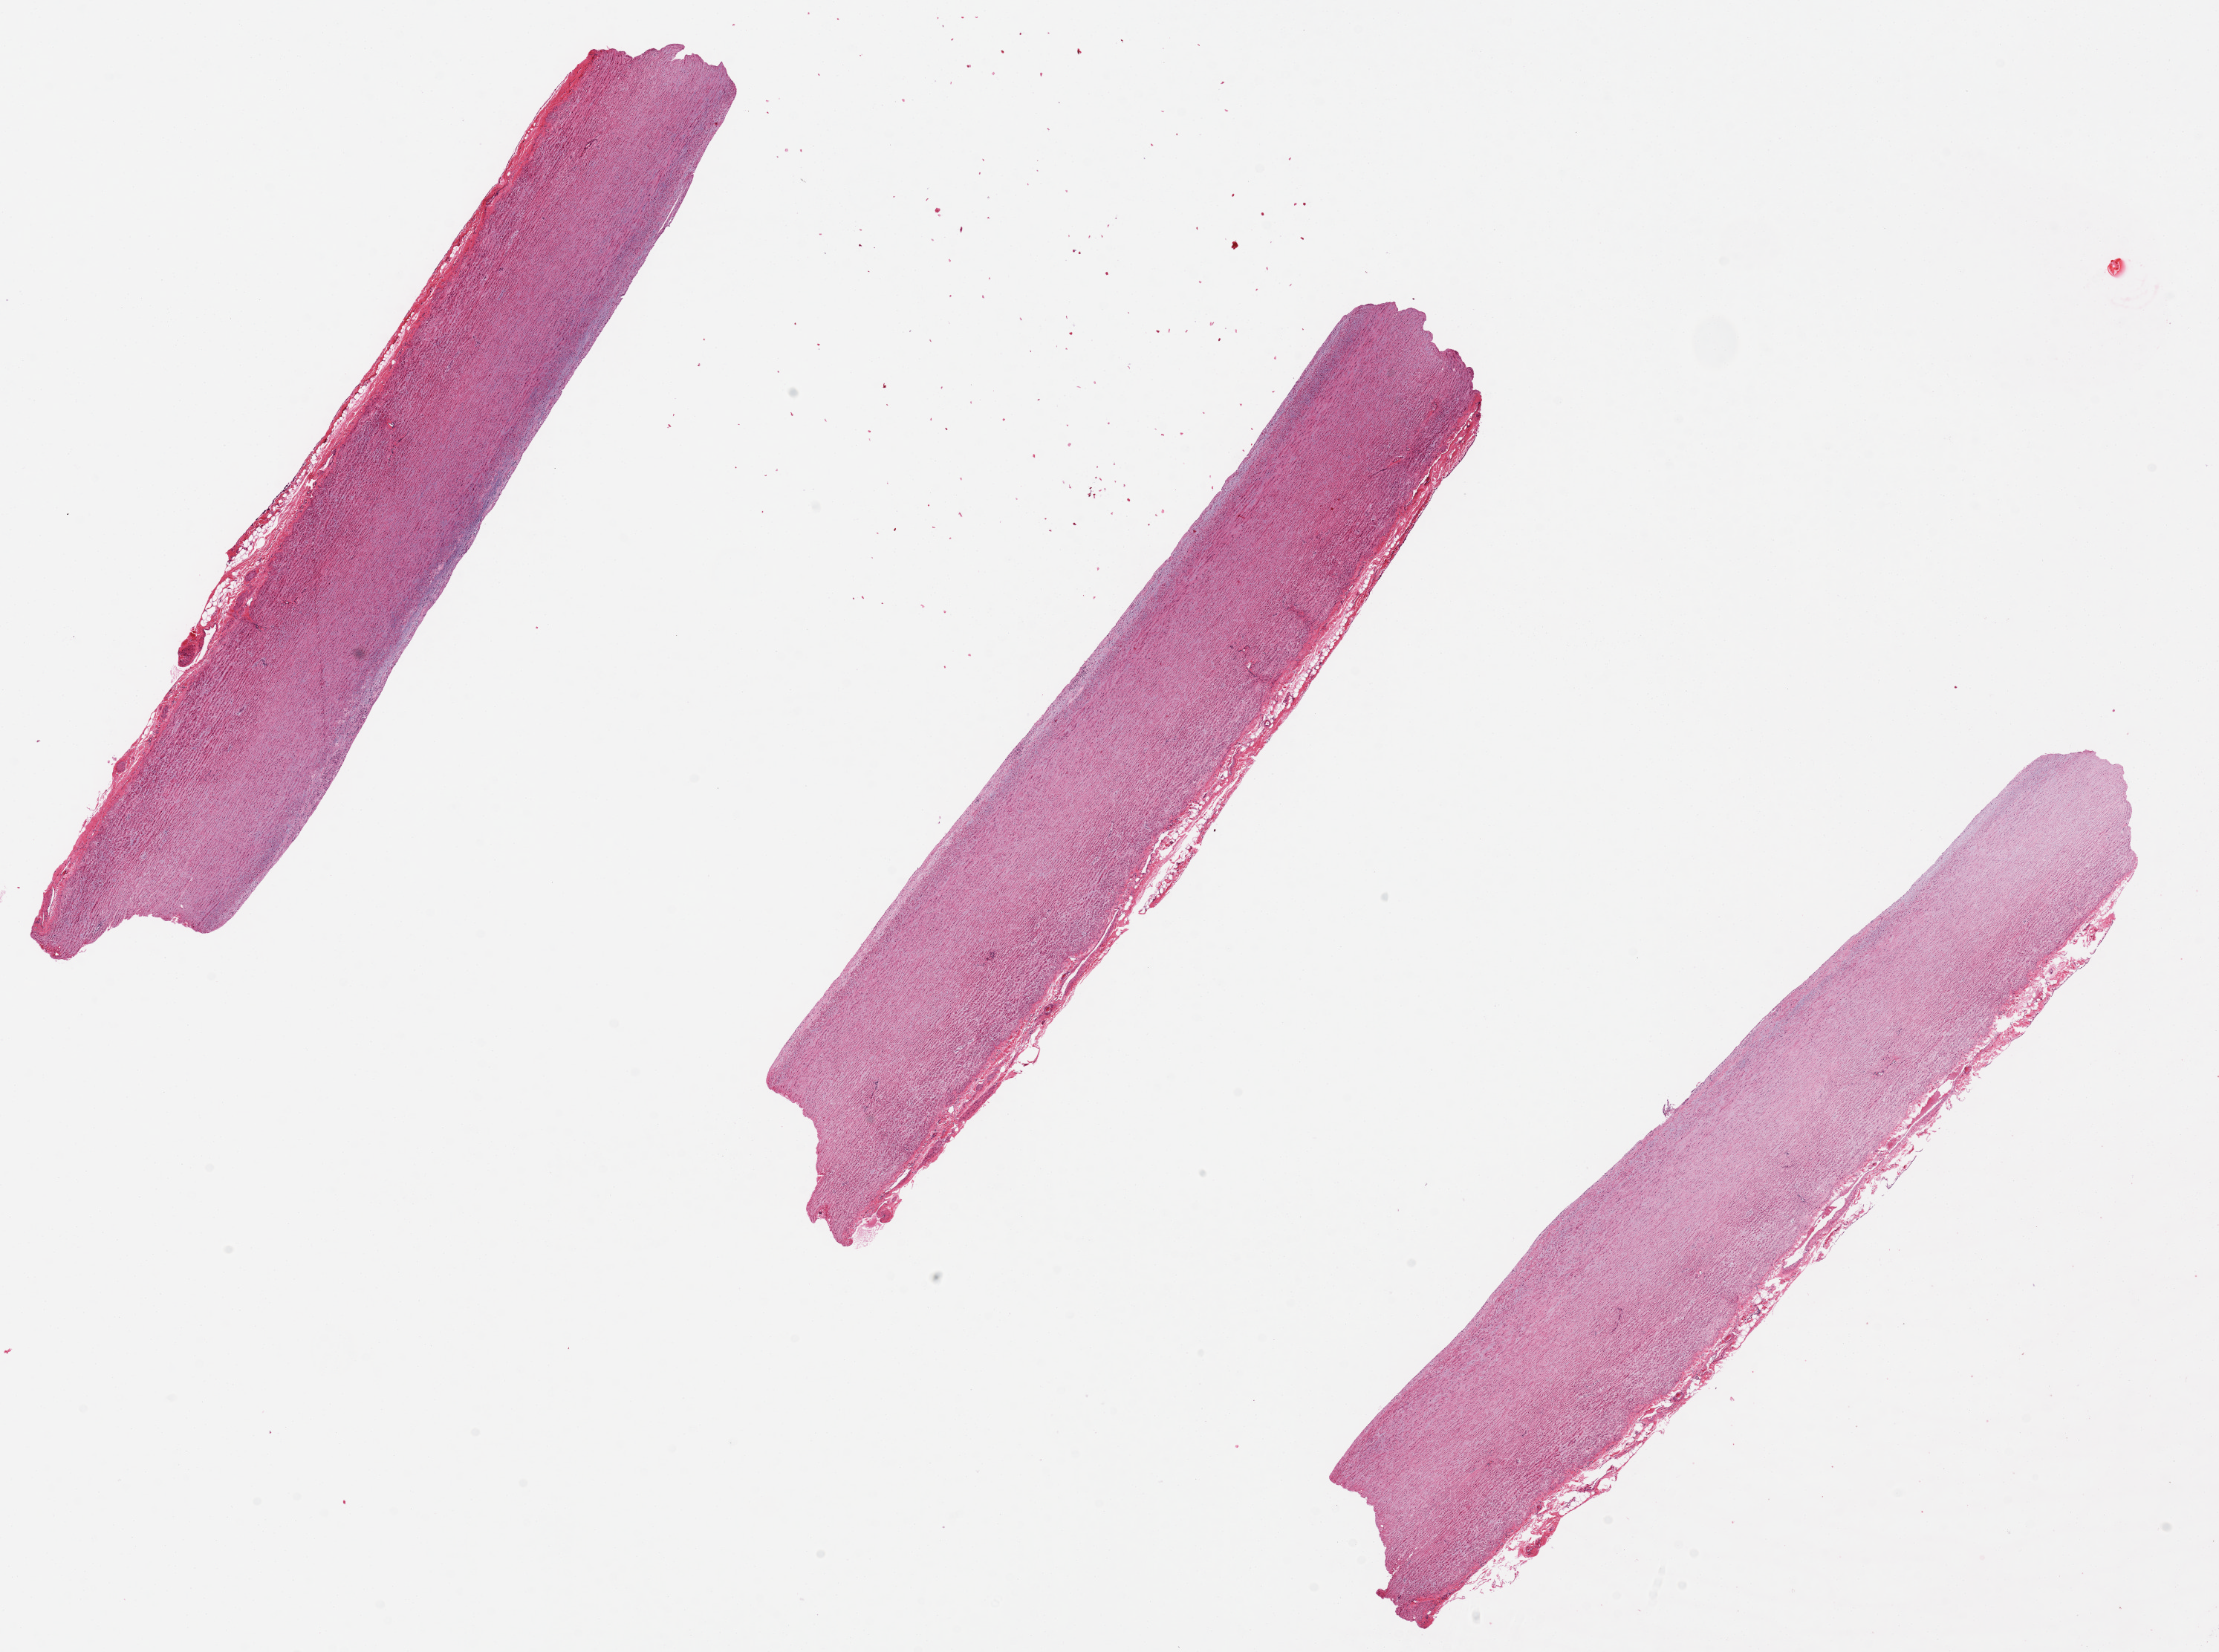
Digitized hematoxylin and eosin (H&E)-stained section — shown as a low-resolution overview of the whole scanned area (about 23.6 x 17.6 mm), PAXgene-fixed, paraffin-embedded tissue, target tissue: aorta, donor tissue sample. Donor: male.
Pathologist's review note for this sample: Specimens average 1.8mm thickness, clean sections.